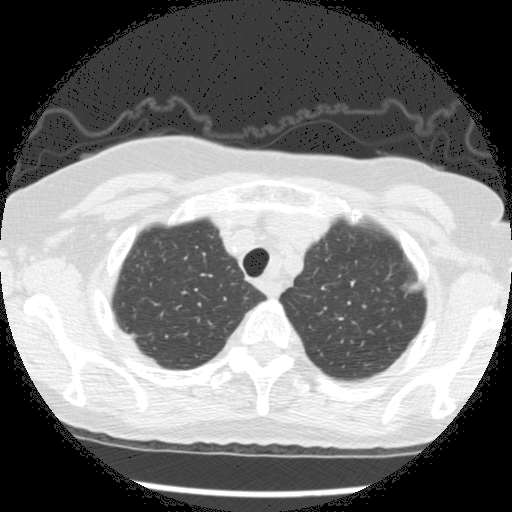
Chest CT (low-dose screening protocol), one axial image; second annual screen; lung window (W 1500 / L -600 HU); standard (soft-tissue) reconstruction kernel (STANDARD); slice 33 of 266 in the series. Female participant, aged 73 years at enrolment. Former smoker at enrolment.
Expert reader's lesion annotation, bounding box (x1, y1, x2, y2) in pixels: (384, 253, 430, 300). The screening reader recorded 3 non-calcified nodules or masses ≥4 mm on this exam (left upper lobe, left upper lobe, left upper lobe); which of them this box marks is not recorded. Lung cancer was diagnosed 49 days after this screen: bronchiolo-alveolar adenocarcinoma, NOS, left upper lobe, well differentiated (G1), stage IA (AJCC 6th edition), 10 mm at pathology.